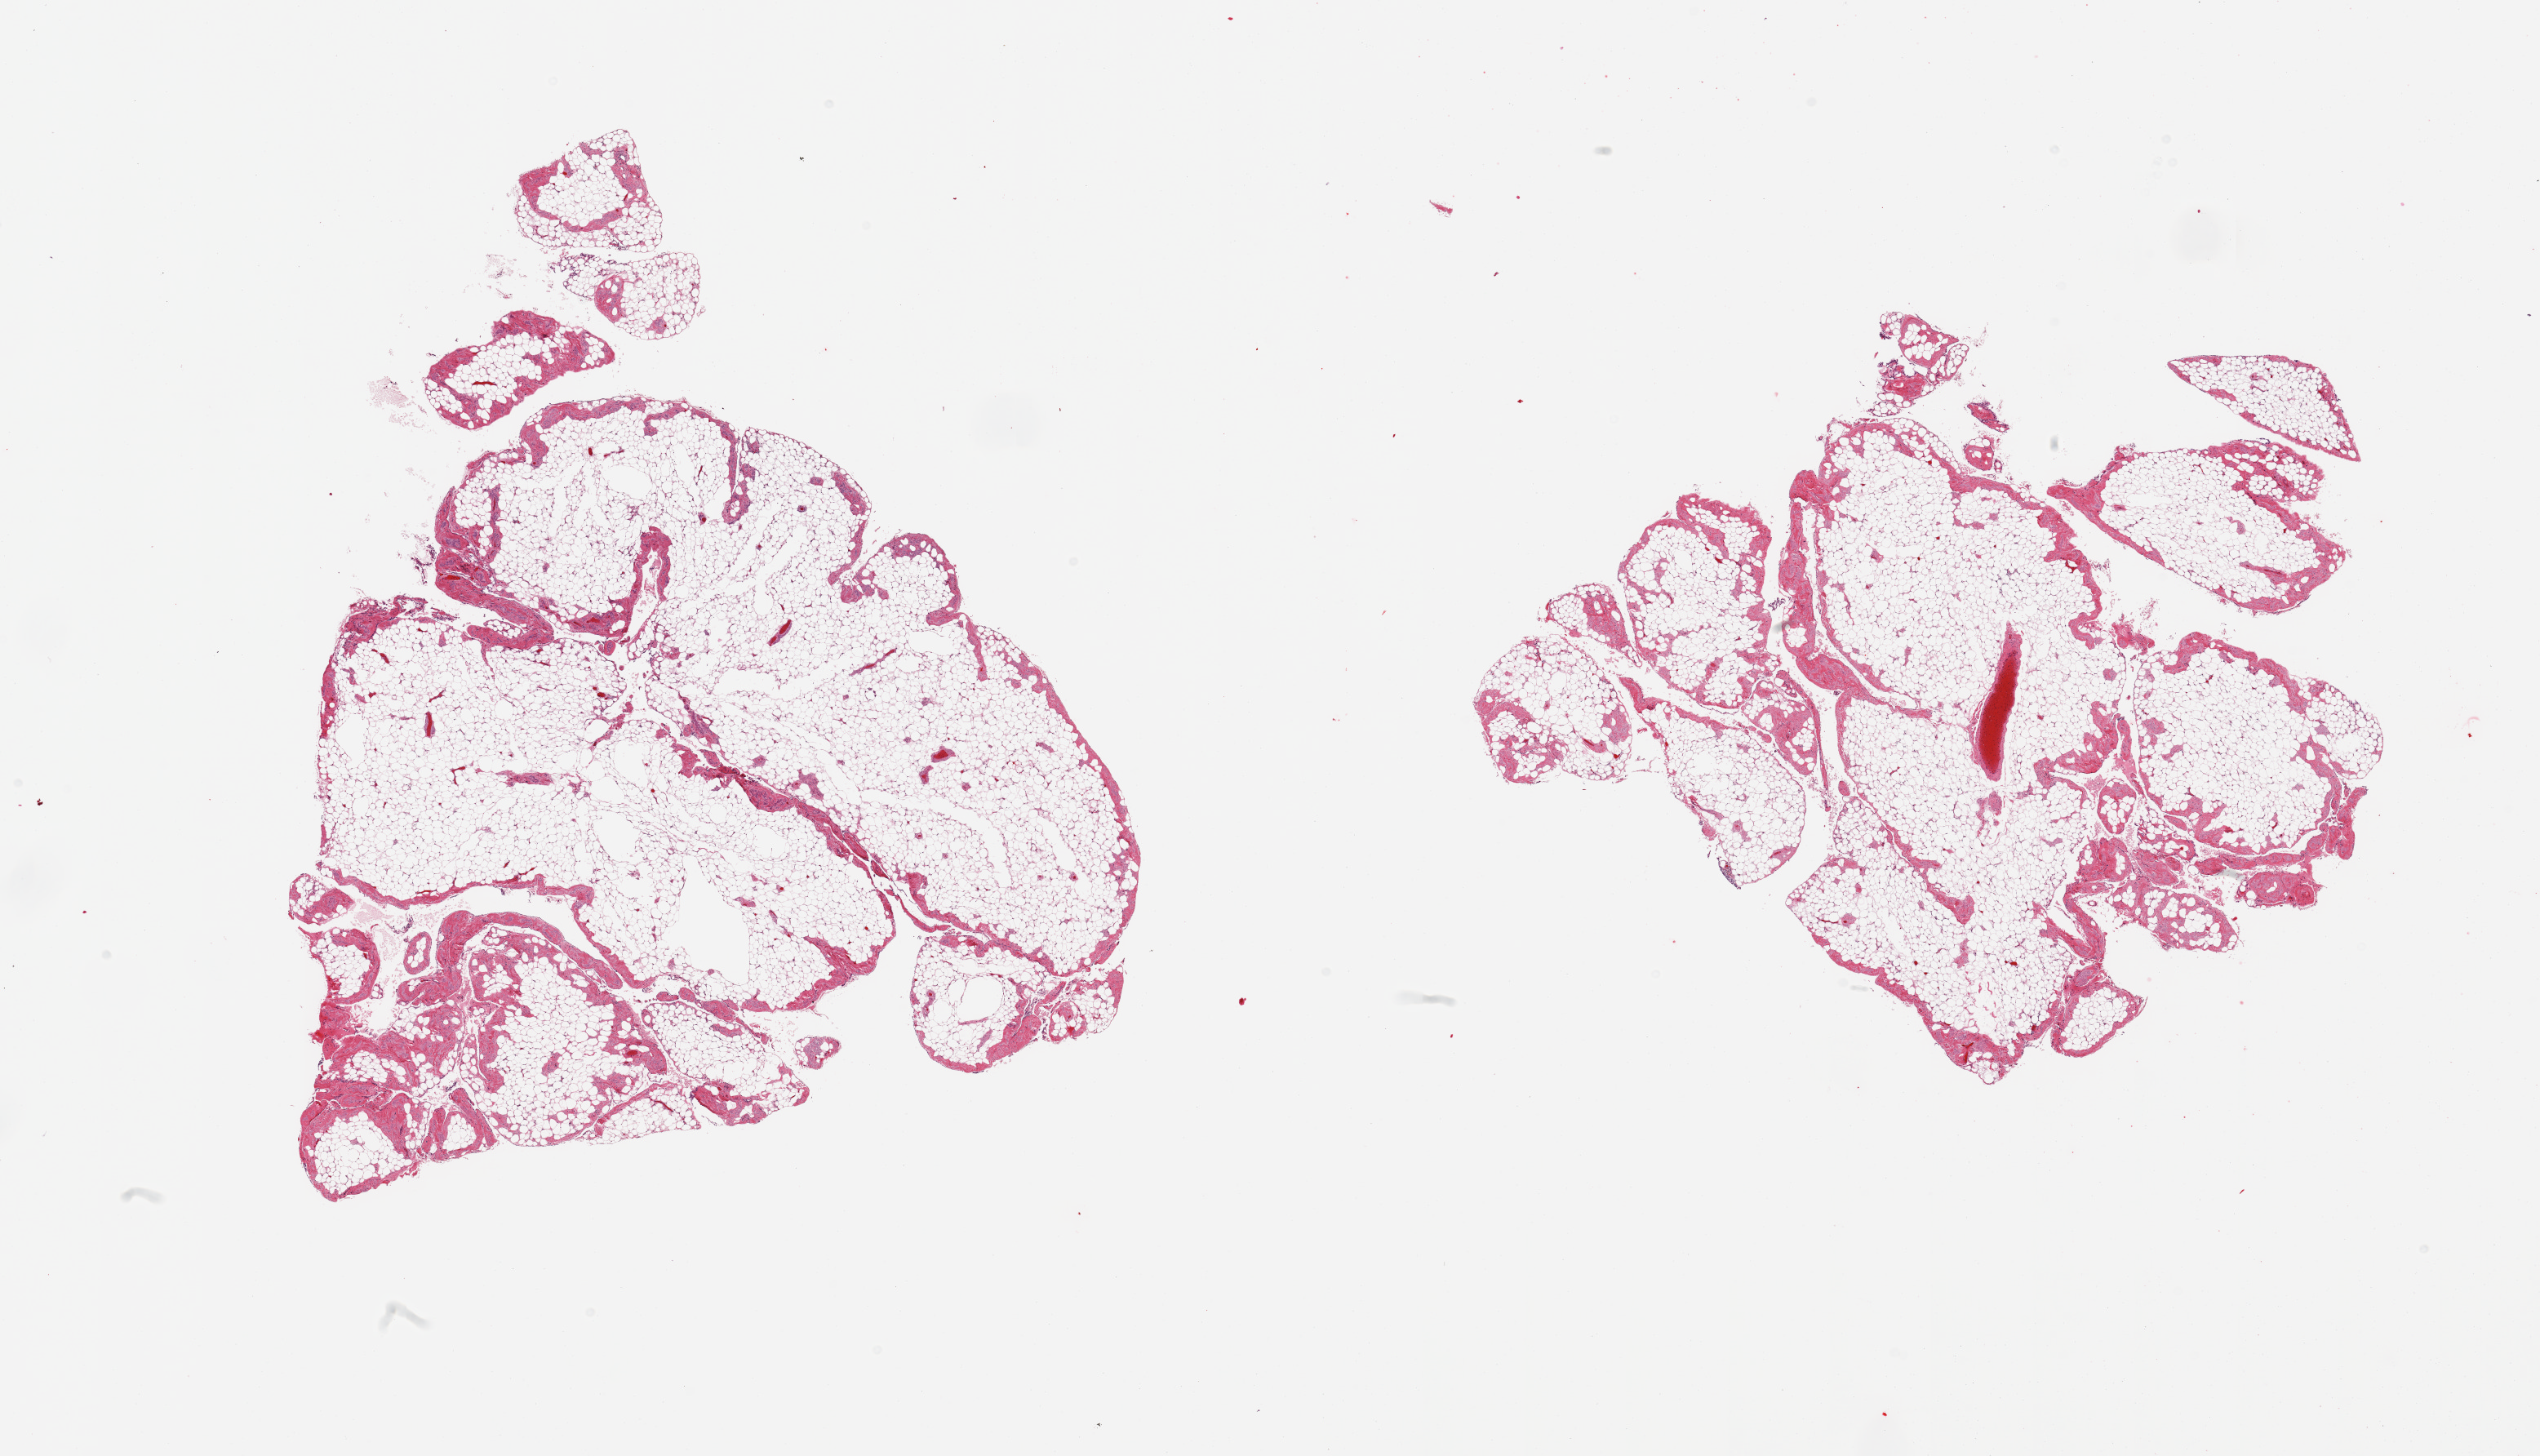
Digitized haematoxylin and eosin-stained section, brightfield, low-resolution overview of the scanned area, about 24.6 x 14.1 mm (from a 20x scan); PAXgene-fixed, paraffin-embedded tissue; target tissue: omentum; tissue donor sample. Male donor.
• pathologist's review note for this sample: 2 pieces; thin submesothelial fibrosis